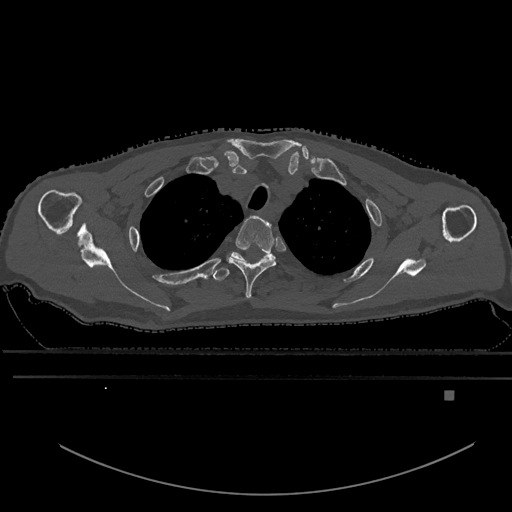
CT including the spine, one axial slice. Slice 486 of 969 in the series (ordered by position). Bone window (W 1800 / L 400 HU). 512 × 512 image matrix. Patient: male, 82 years. Case-level facts recorded for this patient, not image findings: primary cancer: prostate; vertebrae with lytic lesions (as recorded): T11, T9, T8, T2.
Annotated regions visible in this slice (semi-automatic segmentation, software-assisted and operator-edited):
- T2 vertebra: bounding box <227,215,277,299> (left, top, right, bottom; pixels)
- T3 vertebra: <212,253,268,281>